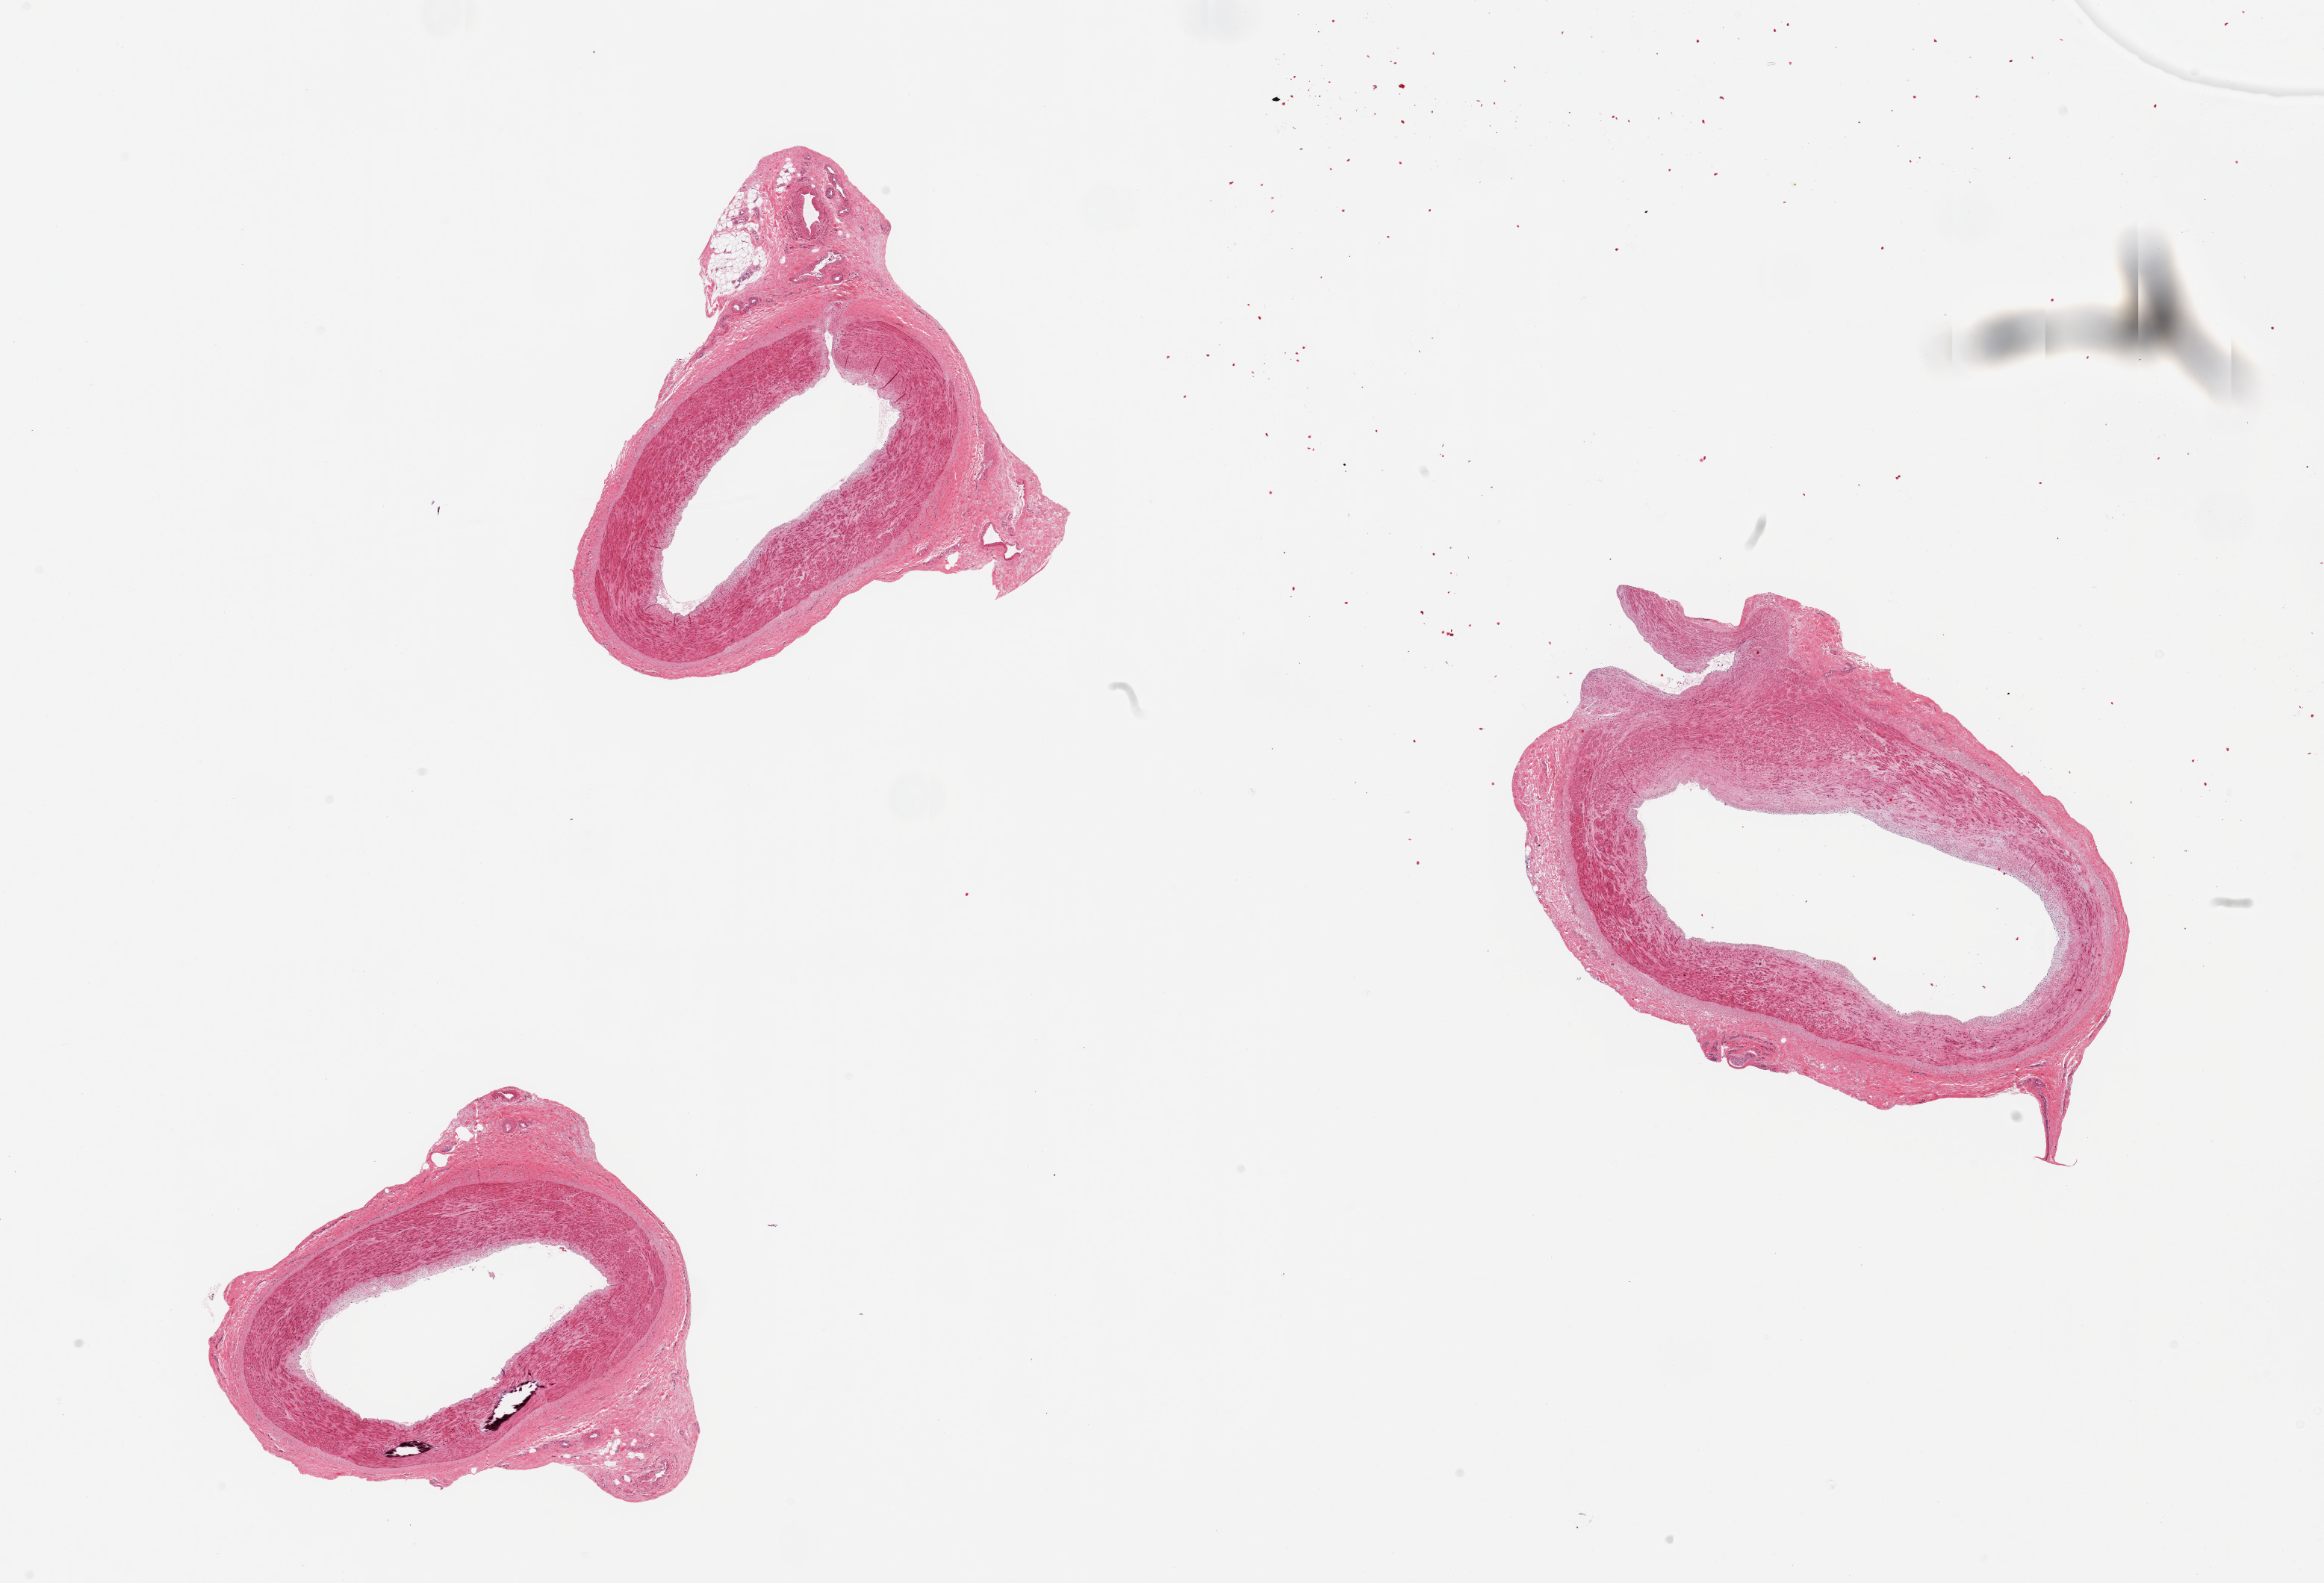
Whole-slide image, hematoxylin and eosin (H&E) stain, brightfield — whole scanned area (about 24.6 x 16.8 mm, acquisition: 20x scan) shown as a low-resolution overview, PAXgene-fixed paraffin-embedded (PFPE) section, target tissue: tibial artery, donor tissue sample. Donor: male.
Reviewer comment on this tissue sample: 3 pieces, no atherosis, clean specimens.